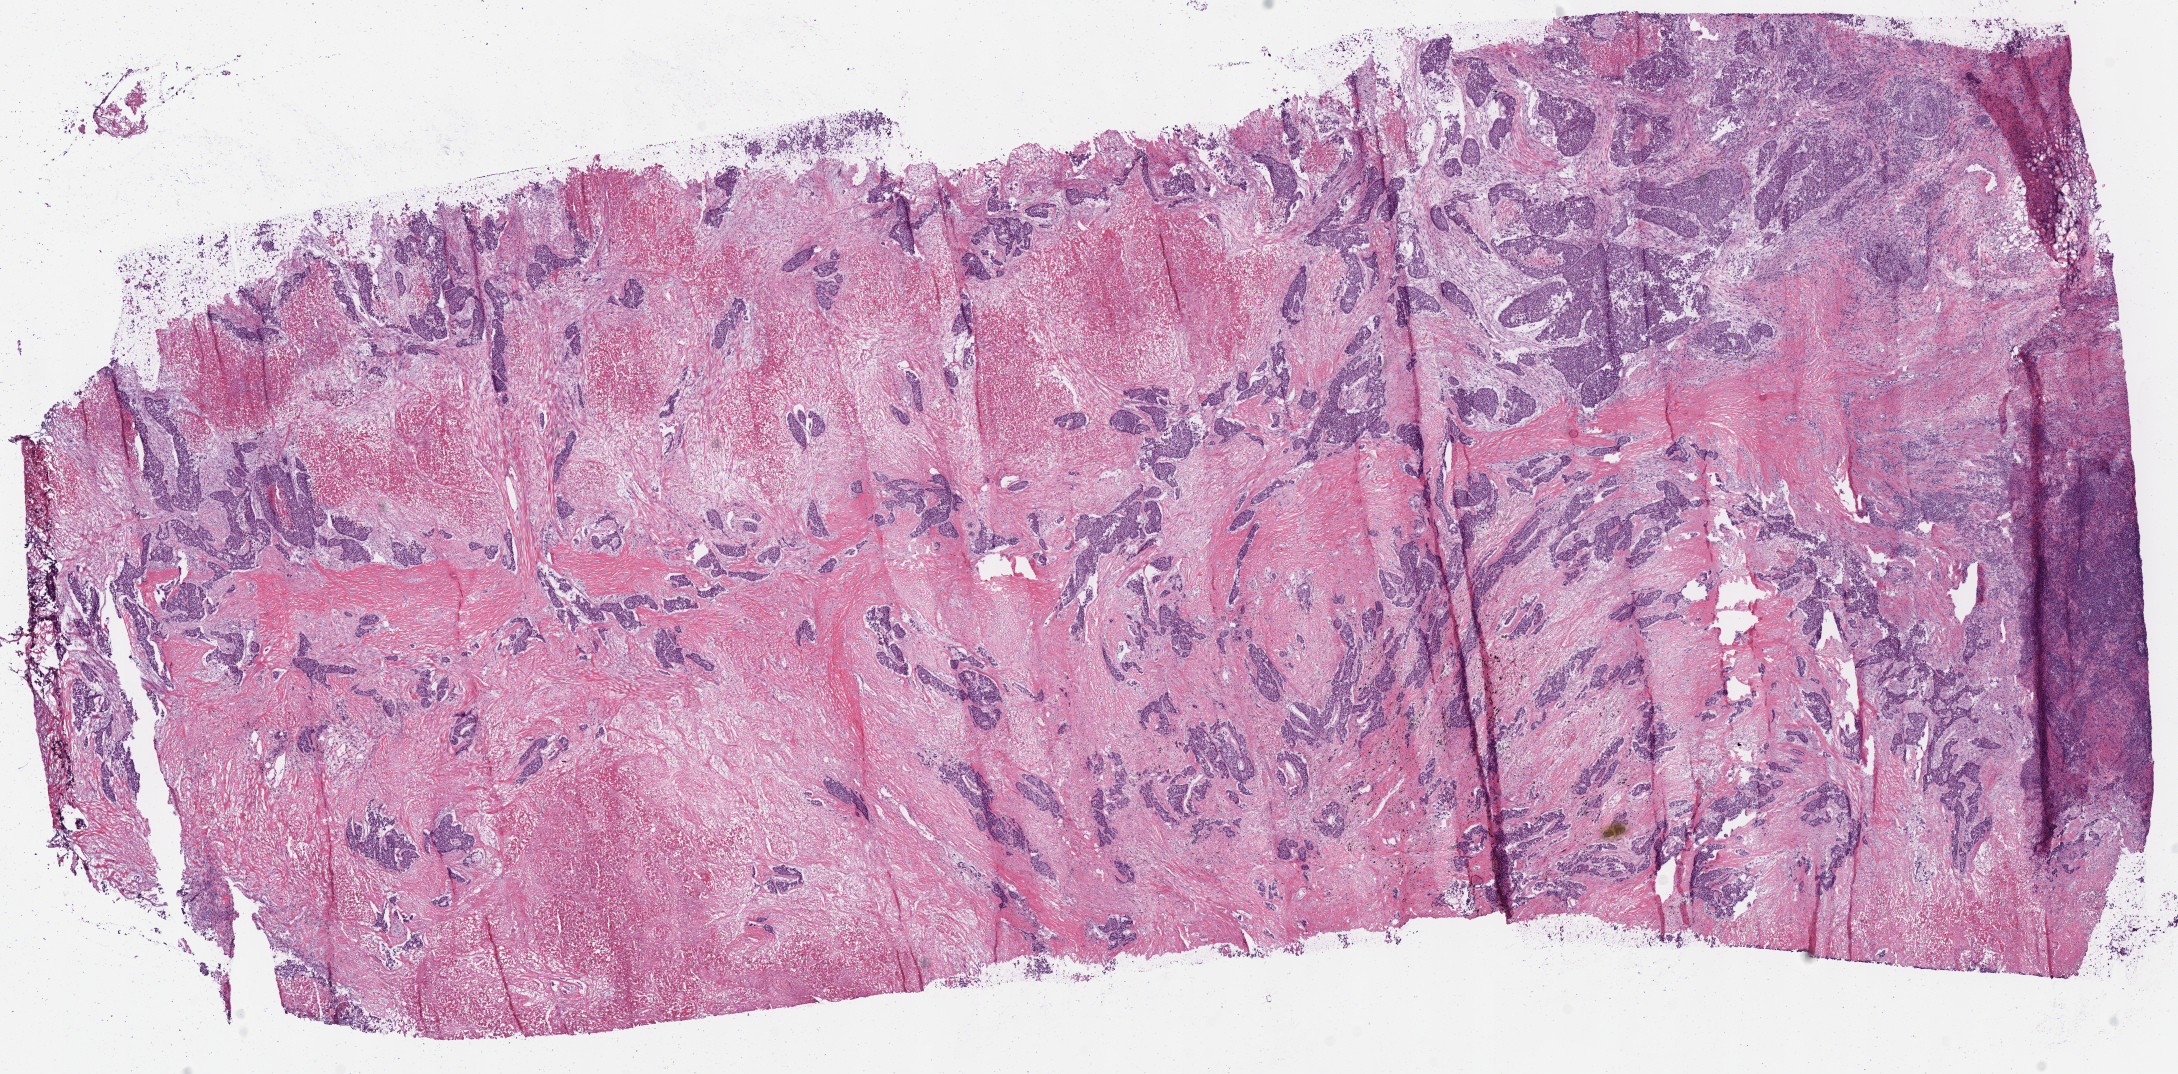
Whole-slide histology image, H&E, shown as a low-resolution overview of the whole scanned area (about 17.1 x 8.4 mm, acquisition: 40x scan); frozen section; primary tumour sample from the lung. Male patient; age at initial diagnosis 73 years. Composition of this section per pathologist review: tumour cells 85%, tumour nuclei 70%, normal cells 0%, stromal cells 0%, necrosis 15%. Inflammatory infiltration, as recorded: lymphocyte infiltration 5%, monocyte infiltration 0%, neutrophil infiltration 0%.
Pathologic diagnosis: Adenocarcinoma, NOS (upper lobe, lung). AJCC pathologic stage: IIB (7th edition).